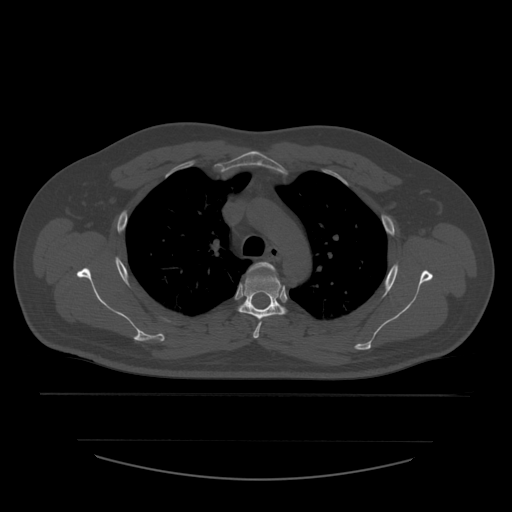
CT including the spine, one axial slice; slice 420 of 532 in the series (ordered by position); 120 kVp; bone window (W 1800 / L 400 HU); 1.25 mm slice thickness; 512 × 512 image matrix, field of view 441 × 441 mm. Patient age 44 years. From the clinical record (not read from this slice): primary cancer: soft tissue sarcoma.
Annotated regions visible in this slice (semi-automatic segmentation, software-assisted and operator-edited):
- T3 vertebra: bounding box [x1, y1, x2, y2] px = [247, 262, 276, 339]
- T4 vertebra: [239, 268, 287, 319]